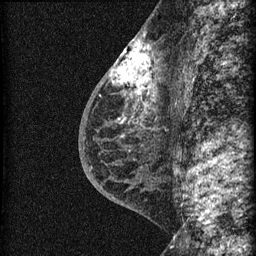
Breast MRI (dynamic contrast-enhanced), one sagittal slice; dynamic contrast-enhanced series, image 2 of 3 at this slice position (ordered by acquisition); 1.5 T; TE 4.2 ms, TR 22.7 ms; 1.5 mm slice thickness; 256 × 256 image matrix, field of view 180 × 180 mm. Female patient, age 48 years. Case-level facts recorded for this patient, not image findings: setting: breast cancer imaged before/during neoadjuvant chemotherapy; receptor status: triple-negative.
Annotated regions visible in this slice (semi-automatic segmentation, software-assisted and operator-edited):
- analysis volume of interest (the breast-tissue region the enhancement analysis was run in; not a lesion): bounding box [x1, y1, x2, y2] px = [115, 34, 169, 162]
- tumour enhancement mask (voxels above the 90 % enhancement threshold inside the analysis volume of interest): [115, 36, 154, 93]